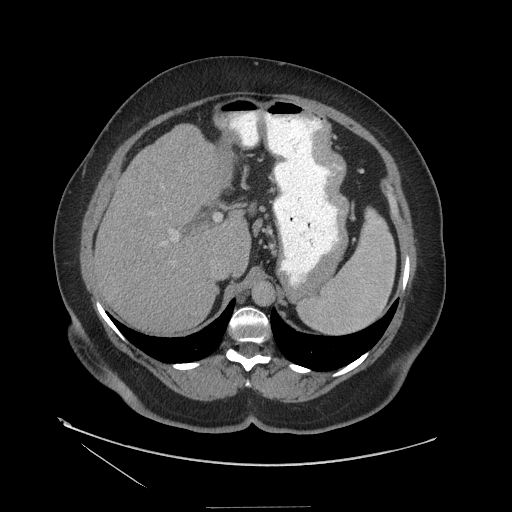
Contrast-enhanced abdominal CT (liver protocol), one axial slice; position 80 of 127 along the scan axis; reconstruction kernel STANDARD; soft-tissue window (W 400 / L 40 HU); 512 × 512 image matrix. From the clinical record (not read from this slice): diagnosis: hepatocellular carcinoma (patient treated with transarterial chemoembolisation; whether this scan precedes or follows treatment is not stated here); TNM stage (as recorded): Stage-II; Child-Pugh class: A; tumour differentiation: well differentiated.
Structures marked on this image (semi-automatic segmentation, software-assisted and operator-edited):
- liver parenchyma outside the tumour (the mass and vessels are separate outlines, so this box may not span the whole liver): box from (x=94, y=114) to (x=258, y=332) px
- liver vessels: (x=244, y=112)–(x=258, y=124)